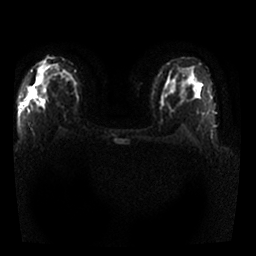
Breast MRI, one axial slice. Position 17 of 25 along the scan axis. Diffusion-weighted series; image 2 of 4 stored at this slice position (different b-values; order by instance number). 1.5 T. 256 × 256 image matrix. Female patient.
Outlined on this slice (manually delineated by an expert):
- tumour on diffusion-weighted imaging: bounding box (x1, y1, x2, y2) in pixels: (31, 88, 46, 101)